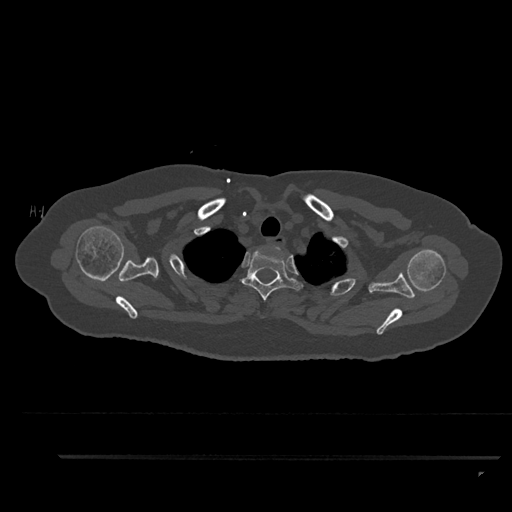
CT including the spine, one axial slice. Position 727 of 797 along the scan axis. Bone window (W 1800 / L 400 HU). 0.5 mm slice thickness. 512 × 512 image matrix, field of view 408 × 408 mm. Female patient, age 44 years. From the clinical record (not read from this slice): primary cancer: renal; vertebrae with lytic lesions (as recorded): L1.
Structures marked on this image (semi-automatically segmented with operator editing):
- T1 vertebra: bounding box <273,246,286,253> (left, top, right, bottom; pixels)
- T2 vertebra: <240,249,304,300>